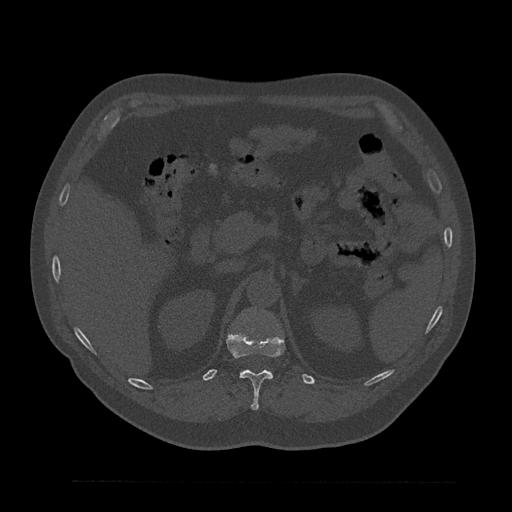
CT including the spine, one axial slice; slice 216 of 797 in the series (ordered by position); reconstruction kernel Br40s/3; 120 kVp; bone window (W 1800 / L 400 HU); 512 × 512 image matrix. Male patient, age 61 years. Case-level facts recorded for this patient, not image findings: primary cancer: prostate.
Structures marked on this image (semi-automatically segmented with operator editing):
- T12 vertebra: box from (x=226, y=332) to (x=285, y=410) px